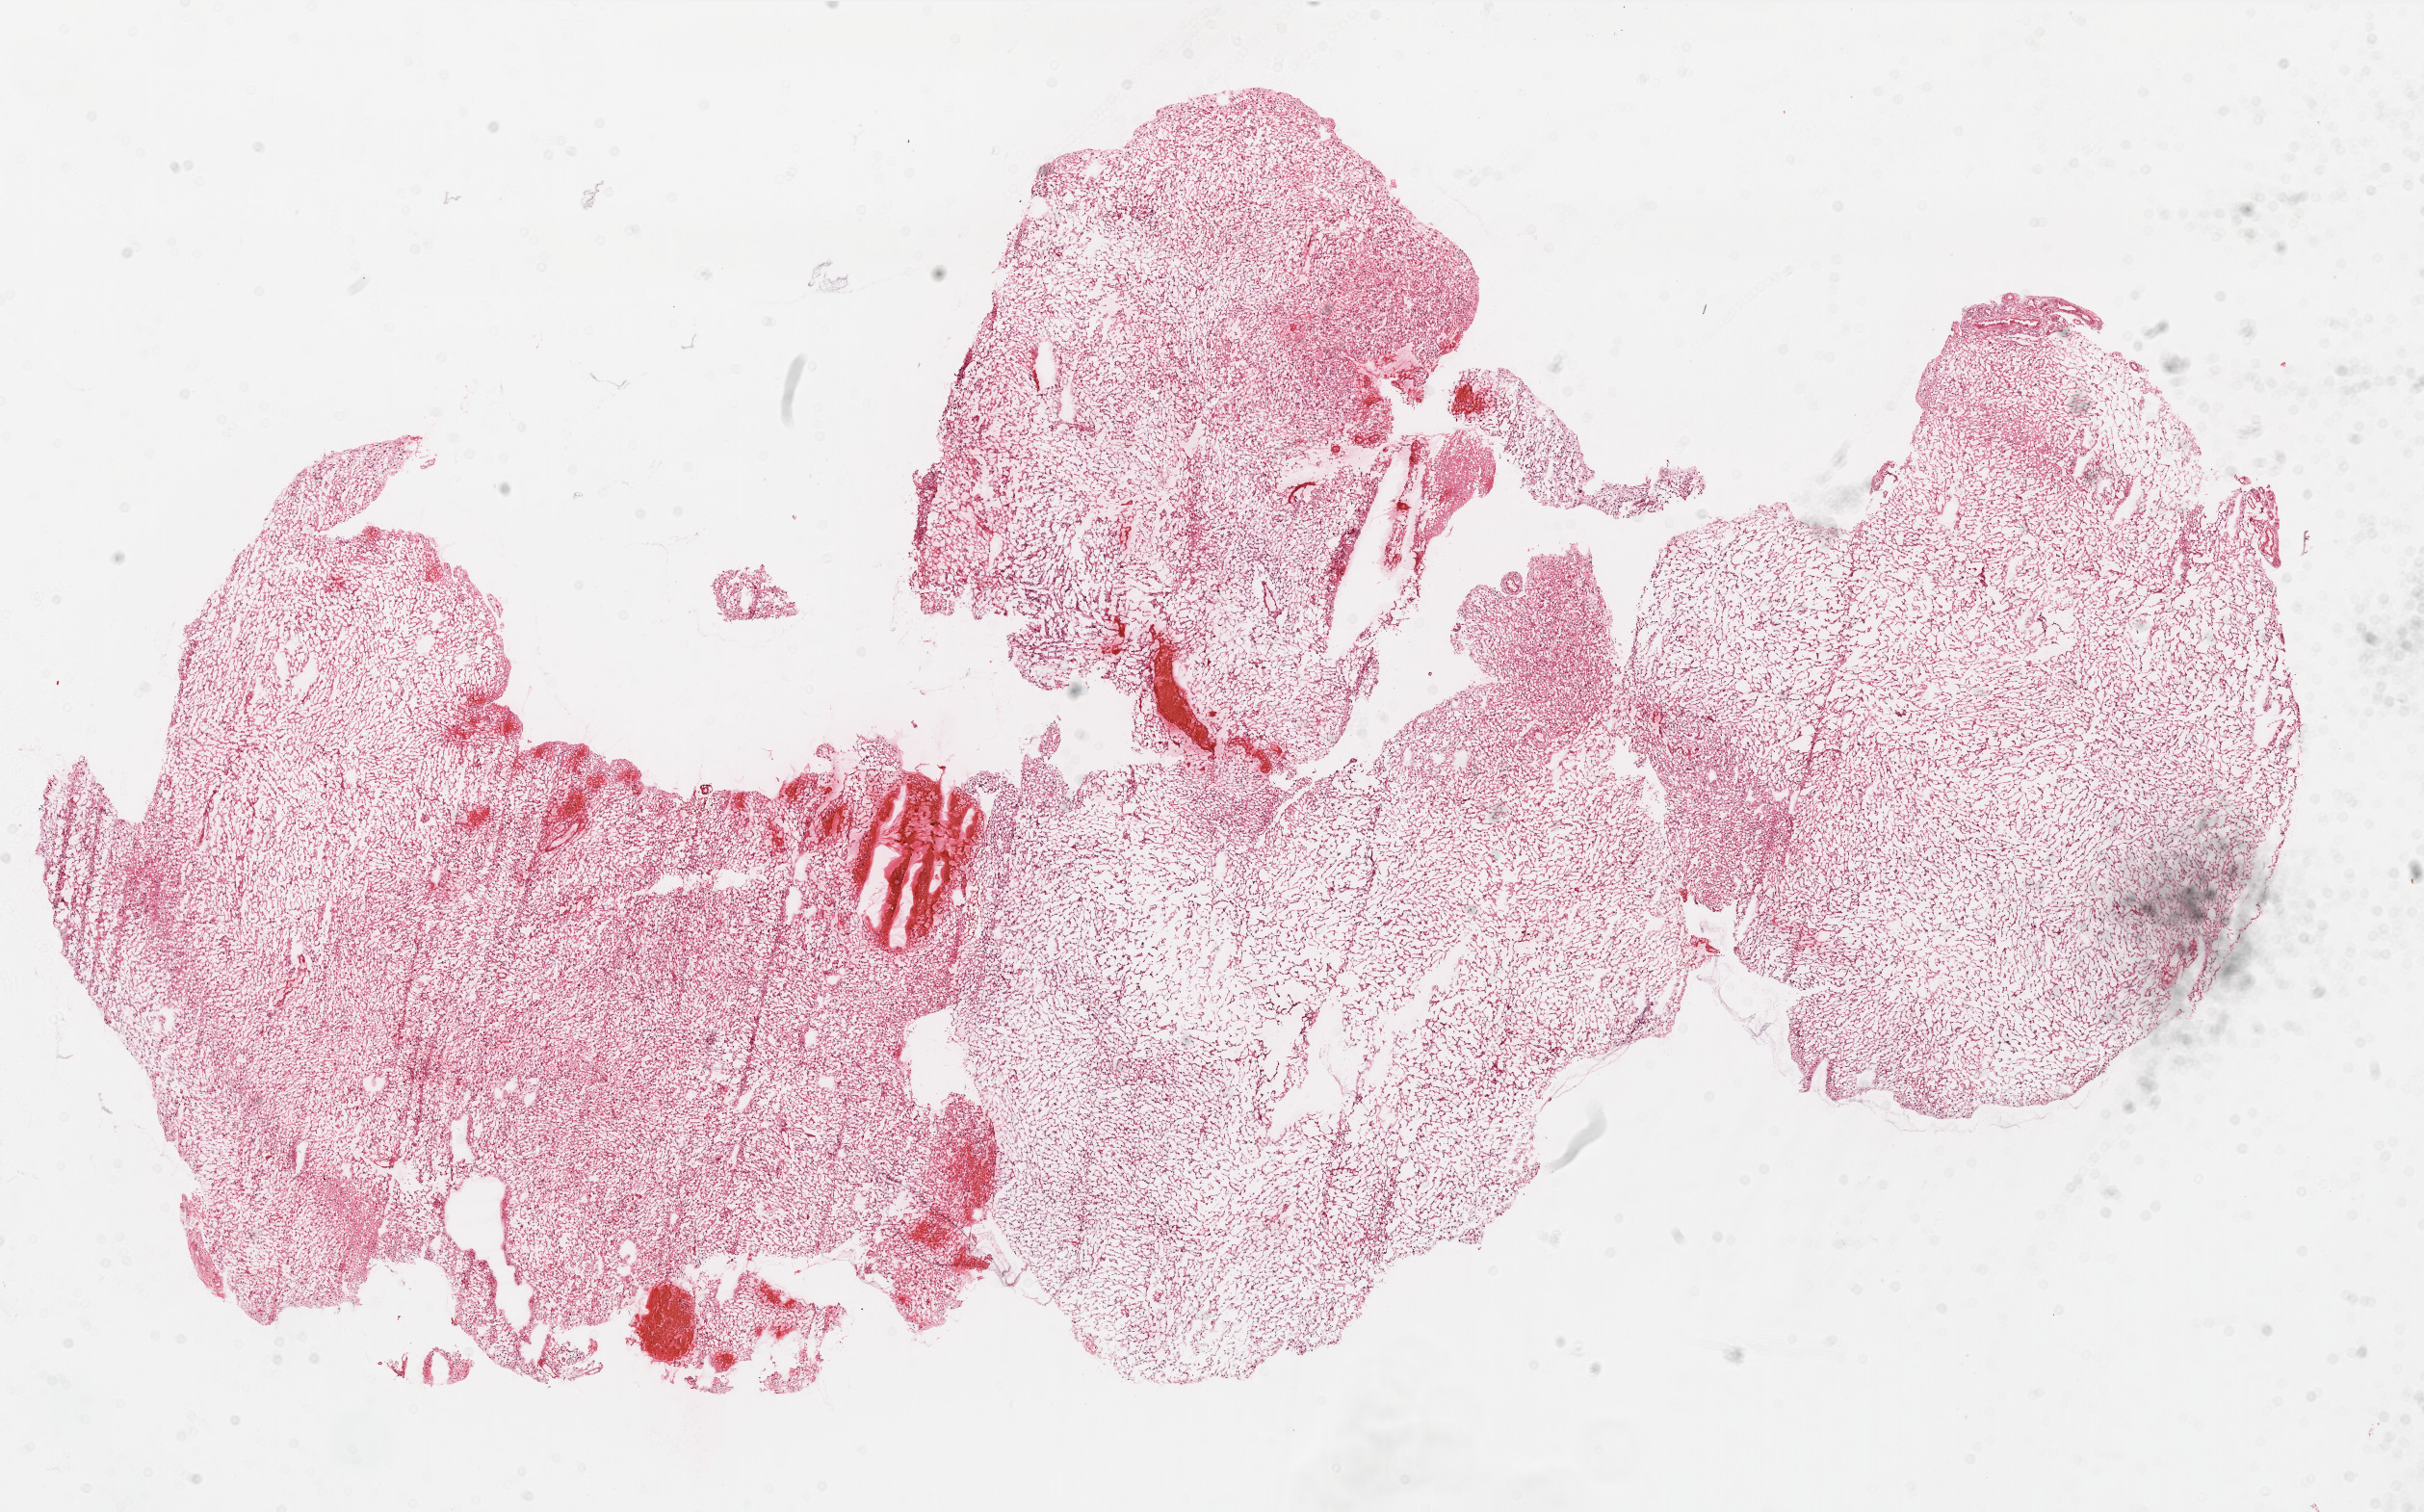
Digitized Hematoxylin and eosin (H&E) stained tissue section (whole slide) — a low-resolution overview of the entire scanned area, about 20.2 x 12.6 mm. Frozen section from the top of the tissue portion. Sample: primary tumour, brain. Female patient; age at initial diagnosis 68 years. Slide review estimates, as recorded: tumour cells 80%, tumour nuclei 100%, normal cells 0%, stromal cells 0%, necrosis 20%.
Diagnosis: Glioblastoma.